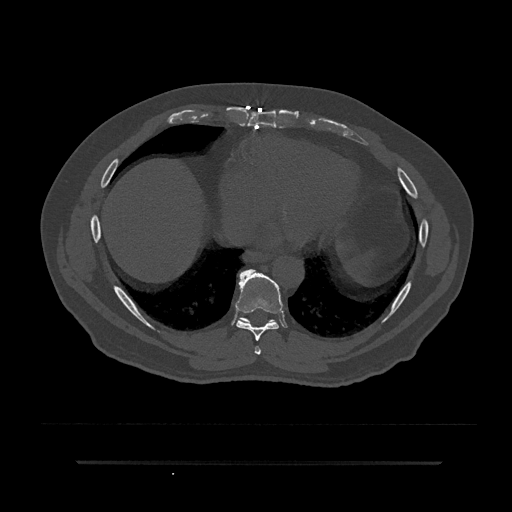
CT including the spine, one axial slice. Reconstruction kernel Br40s/3. 120 kVp. Bone window (W 1800 / L 400 HU). 512 × 512 image matrix. Male patient, age 59 years. From the clinical record (not read from this slice): primary cancer: bile ducts.
Structures marked on this image (semi-automatically segmented with operator editing):
- T7 vertebra: bounding box <254,346,261,355> (left, top, right, bottom; pixels)
- T8 vertebra: <235,269,284,341>
- T9 vertebra: <239,317,274,322>